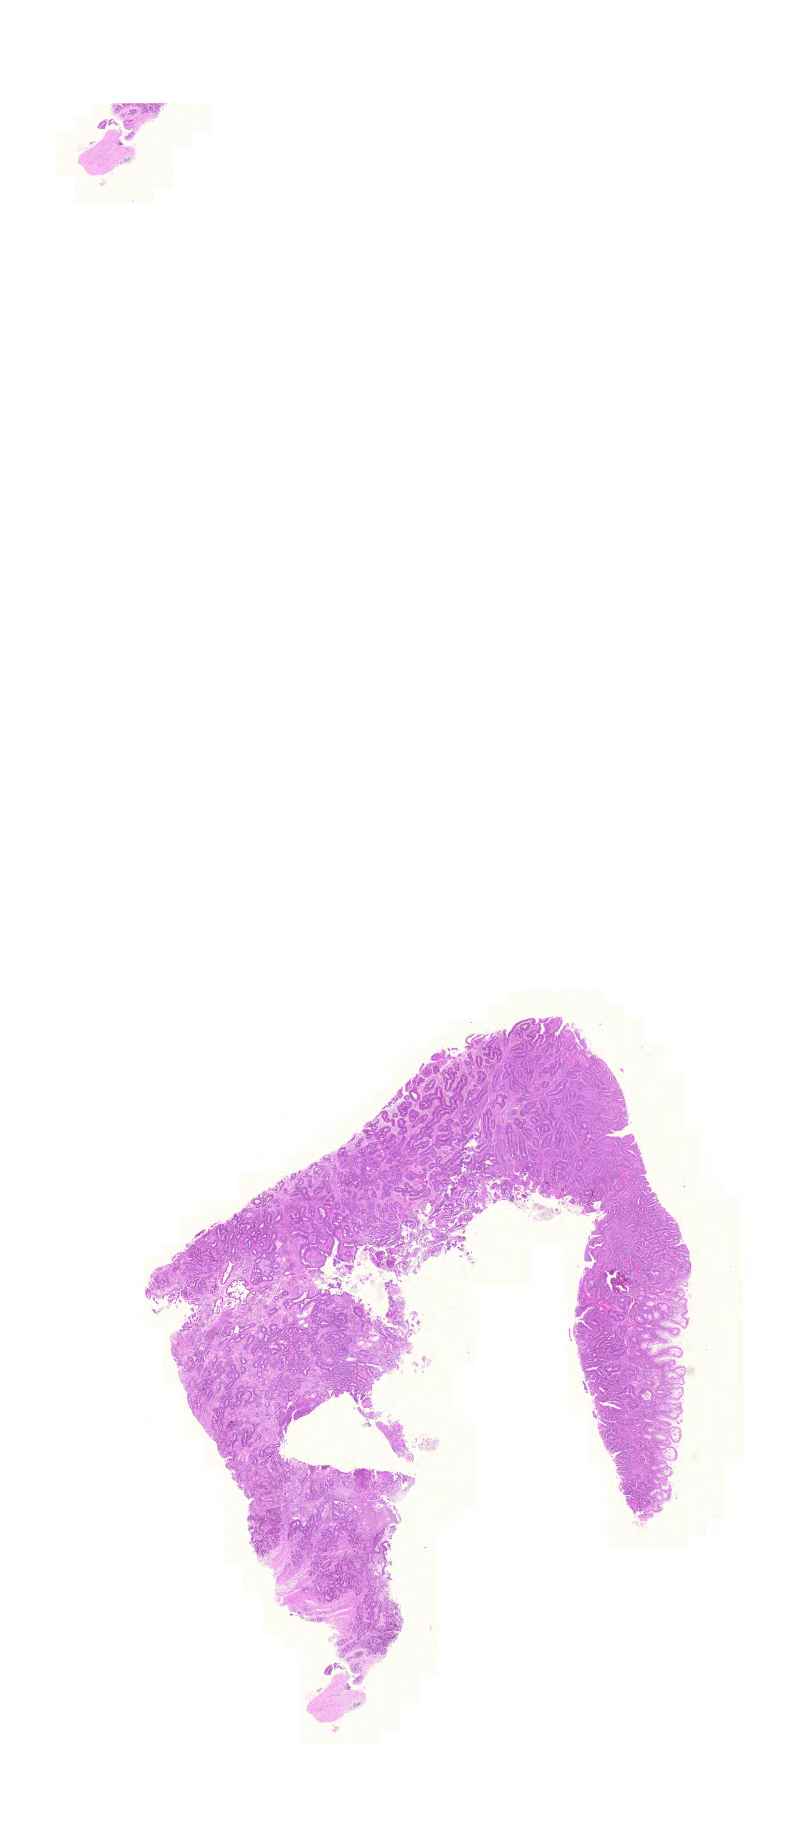
Digitized Hematoxylin and eosin (H&E) stained tissue section (whole slide), a low-resolution overview of the entire scanned area, about 11.7 x 27.3 mm (from a 20x scan). FFPE section. Rectum, primary tumour sample. Male patient; age at initial diagnosis 73 years.
AJCC pathologic stage: IIIB (6th edition). Histologic diagnosis: Adenocarcinoma, NOS.